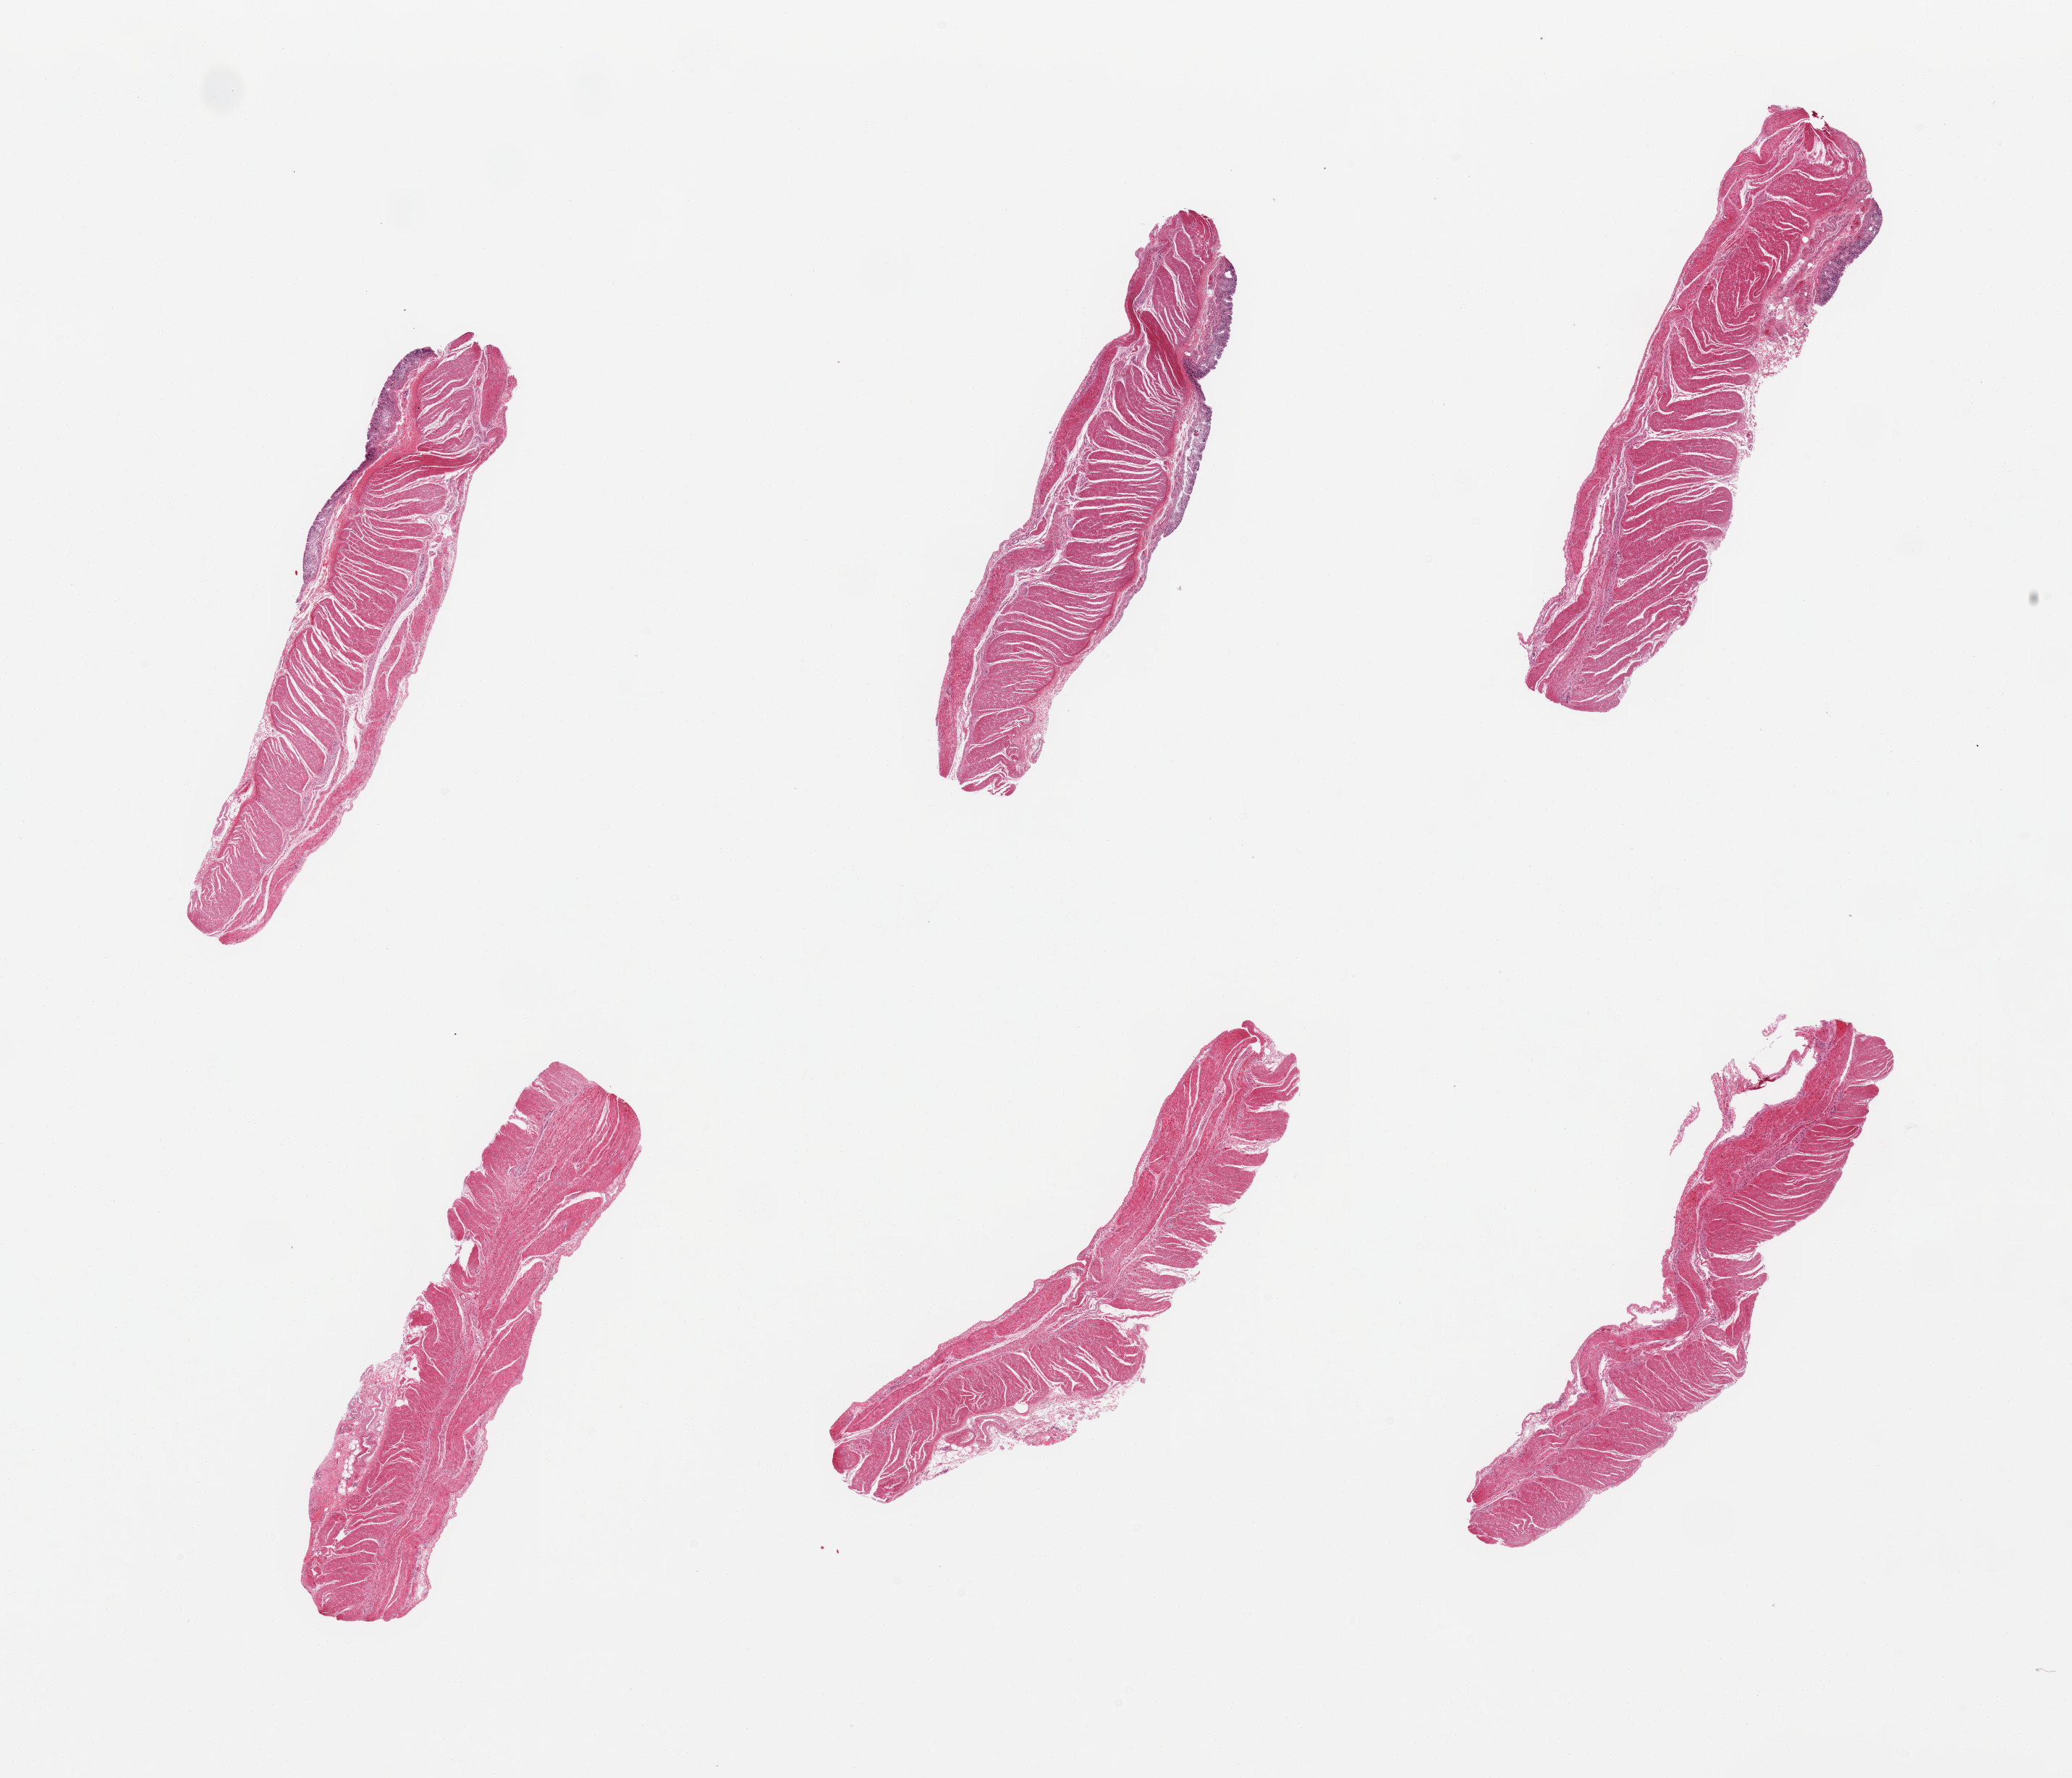
Whole-slide image, hematoxylin and eosin (H&E) stain — a low-resolution overview of the entire scanned area, about 22.6 x 19.4 mm. PAXgene-fixed, paraffin-embedded tissue. Sampled site (target tissue): sigmoid colon. Tissue donor sample.
• pathologist's review note for this sample: 6 pieces; 3 pieces have autolyzed mucosal remnants